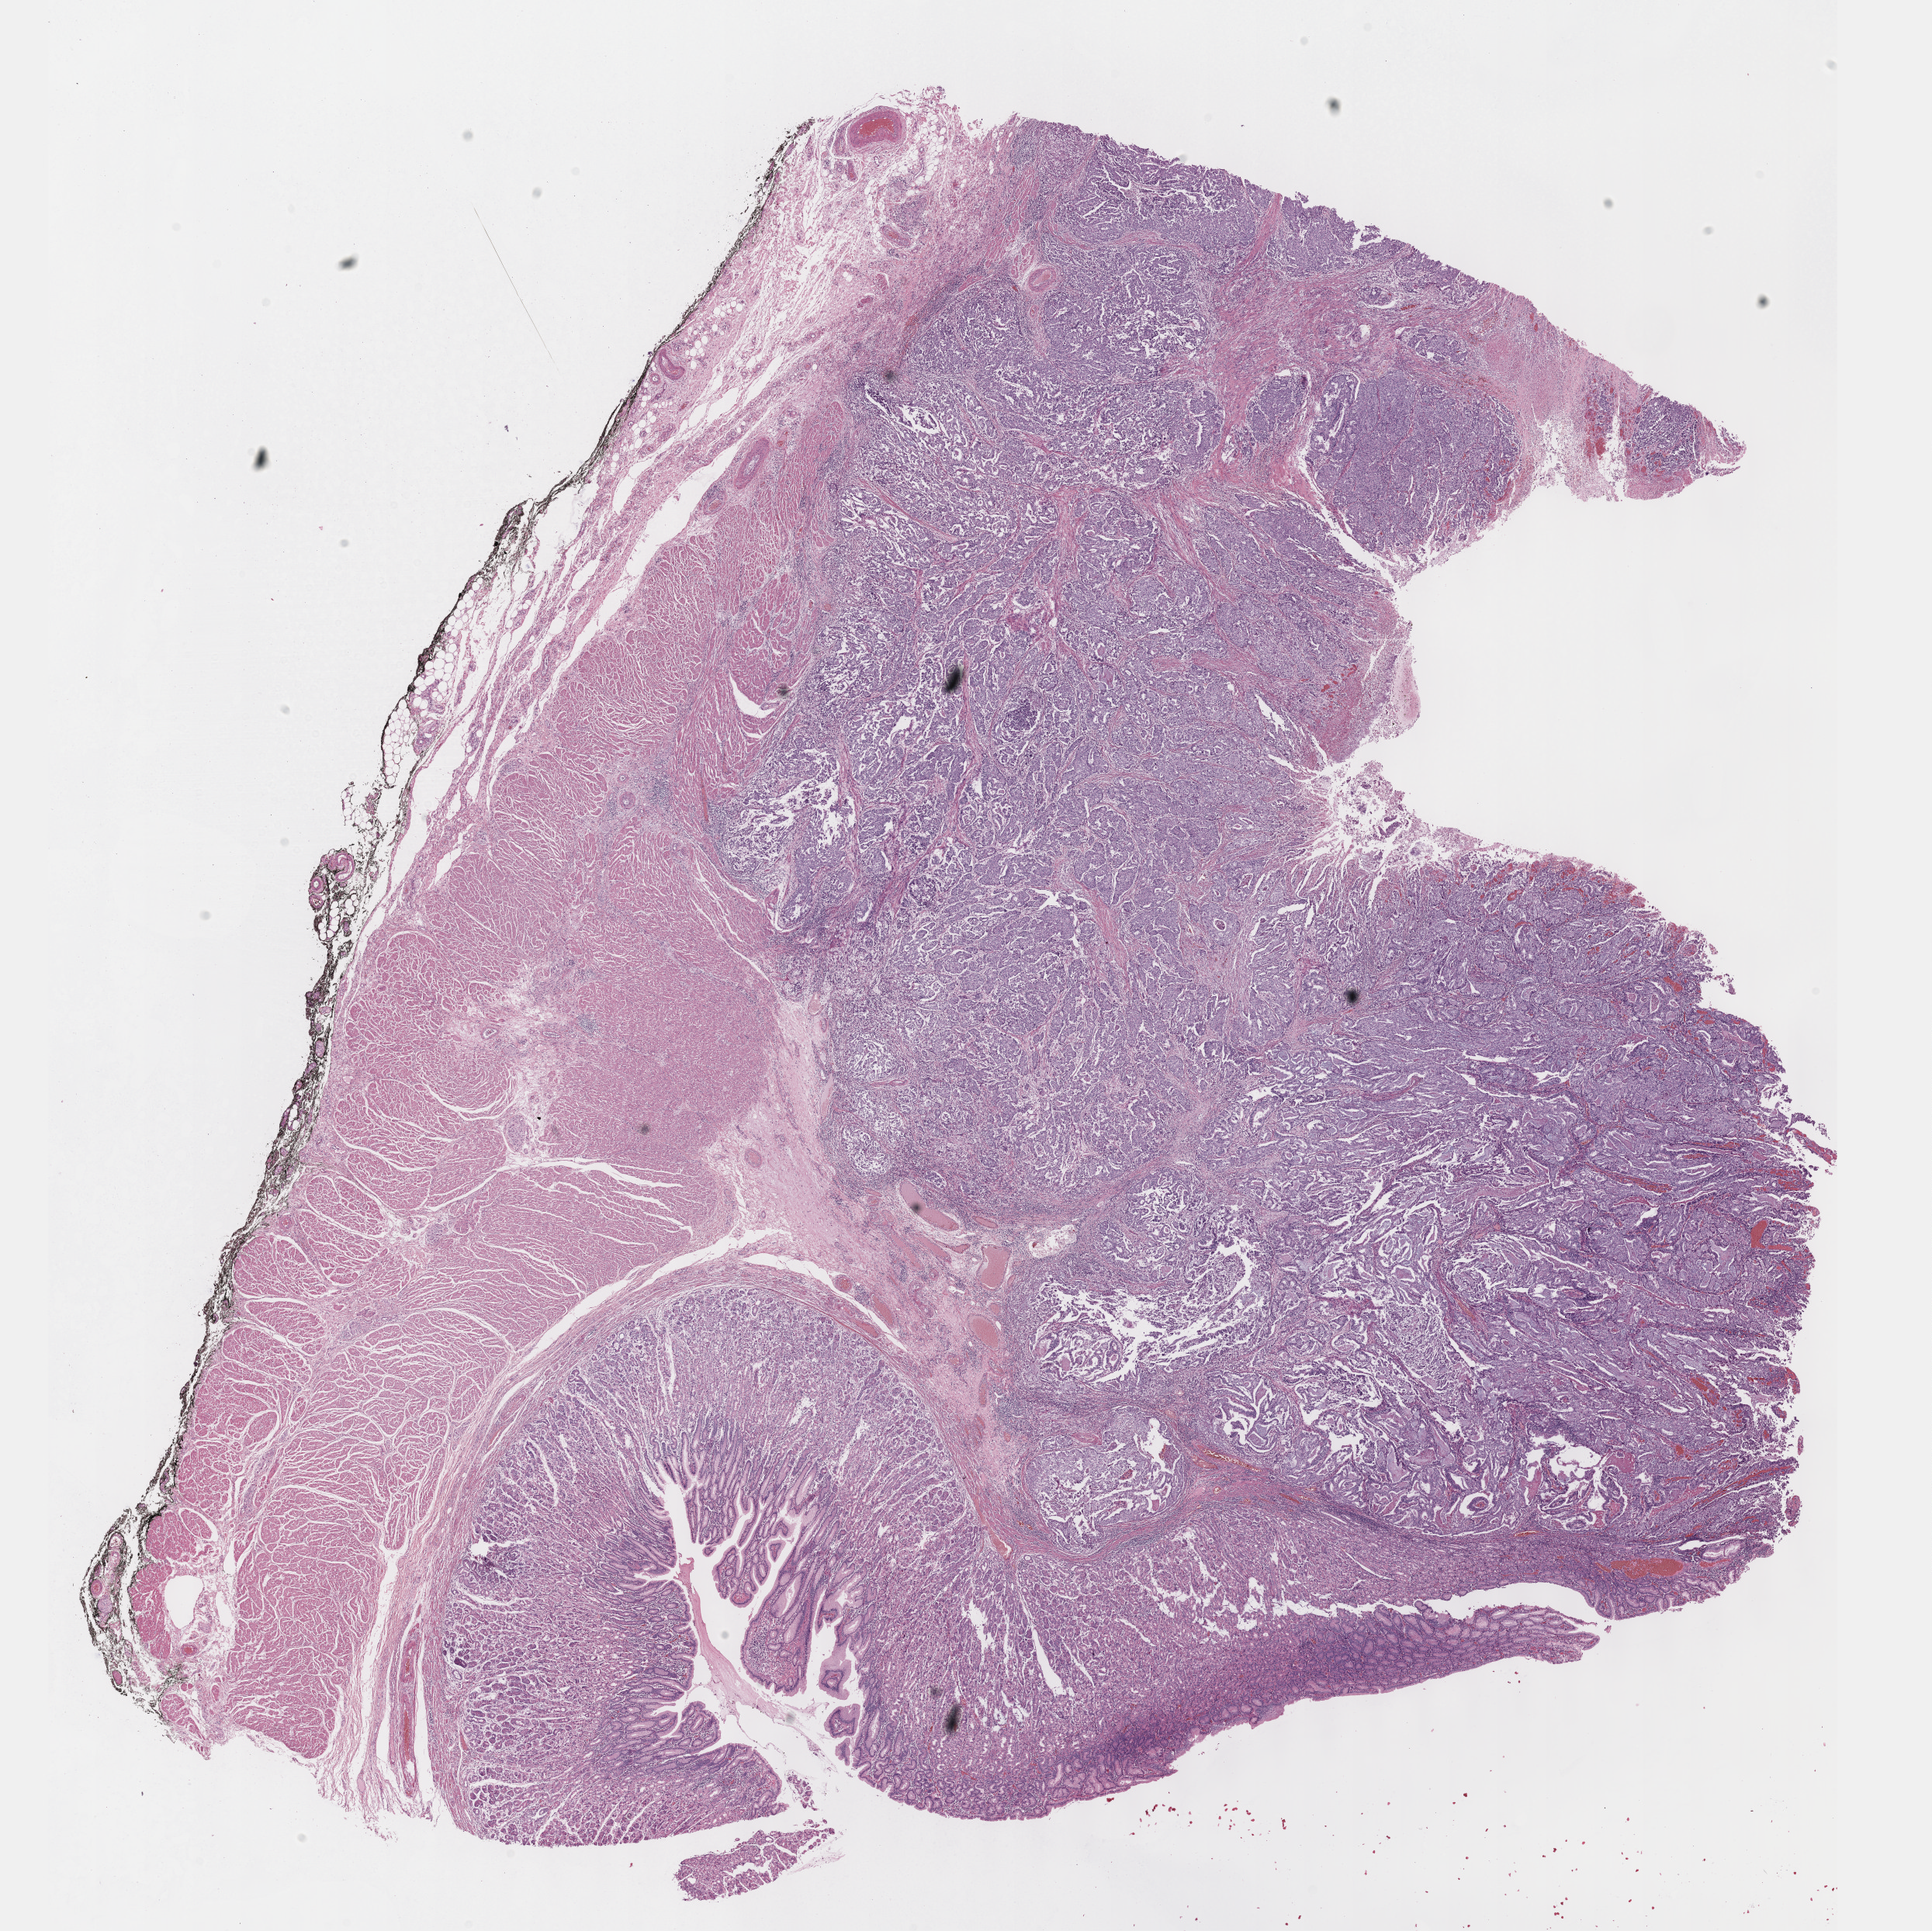
Digitized H&E tissue section (whole slide) — low-resolution overview of the scanned area, about 20.1 x 20.1 mm; FFPE section; primary tumour sample from the stomach. Female, age 69 years at initial diagnosis. Histologic grade: G2 (moderately differentiated).
AJCC pathologic stage: IIA. Pathologic diagnosis: Tubular adenocarcinoma (cardia, NOS). Lymph nodes positive (case pathology): 0 of 27 examined.